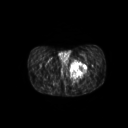
FDG PET of an extremity soft-tissue mass (from a PET/CT study), one axial slice; position 38 of 267 along the scan axis; 128 × 128 image matrix. Male patient, age 59 years. Case-level facts recorded for this patient, not image findings: histological type: pleiomorphic liposarcoma; grade: high; site of the primary tumour: left thigh.
Outlined on this slice (expert contour drawn on MRI and transferred to this co-registered scan by the dataset authors):
- gross tumour volume including surrounding oedema: bounding box <70,60,87,79> (left, top, right, bottom; pixels)
- gross tumour volume (mass): <70,61,86,77>